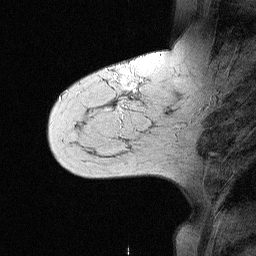
Breast MRI (dynamic contrast-enhanced), one sagittal slice. Position 18 of 64 along the scan axis. Dynamic contrast-enhanced study with each time point stored as its own series, time point 2 of 3 at this slice position (early post-contrast, ordered by acquisition time). 1.5 T. TE 4.5 ms, TR 11 ms. 256 × 256 image matrix. Female patient, age 55 years. Case-level facts recorded for this patient, not image findings: setting: breast cancer imaged before/during neoadjuvant chemotherapy; receptor status: triple-negative.
Structures marked on this image (semi-automatic segmentation, software-assisted and operator-edited):
- analysis volume of interest (the breast-tissue region the enhancement analysis was run in; not a lesion): bounding box (x1, y1, x2, y2) in pixels: (71, 63, 147, 145)
- tumour enhancement mask (voxels above the 90 % enhancement threshold inside the analysis volume of interest): (106, 83, 138, 110)